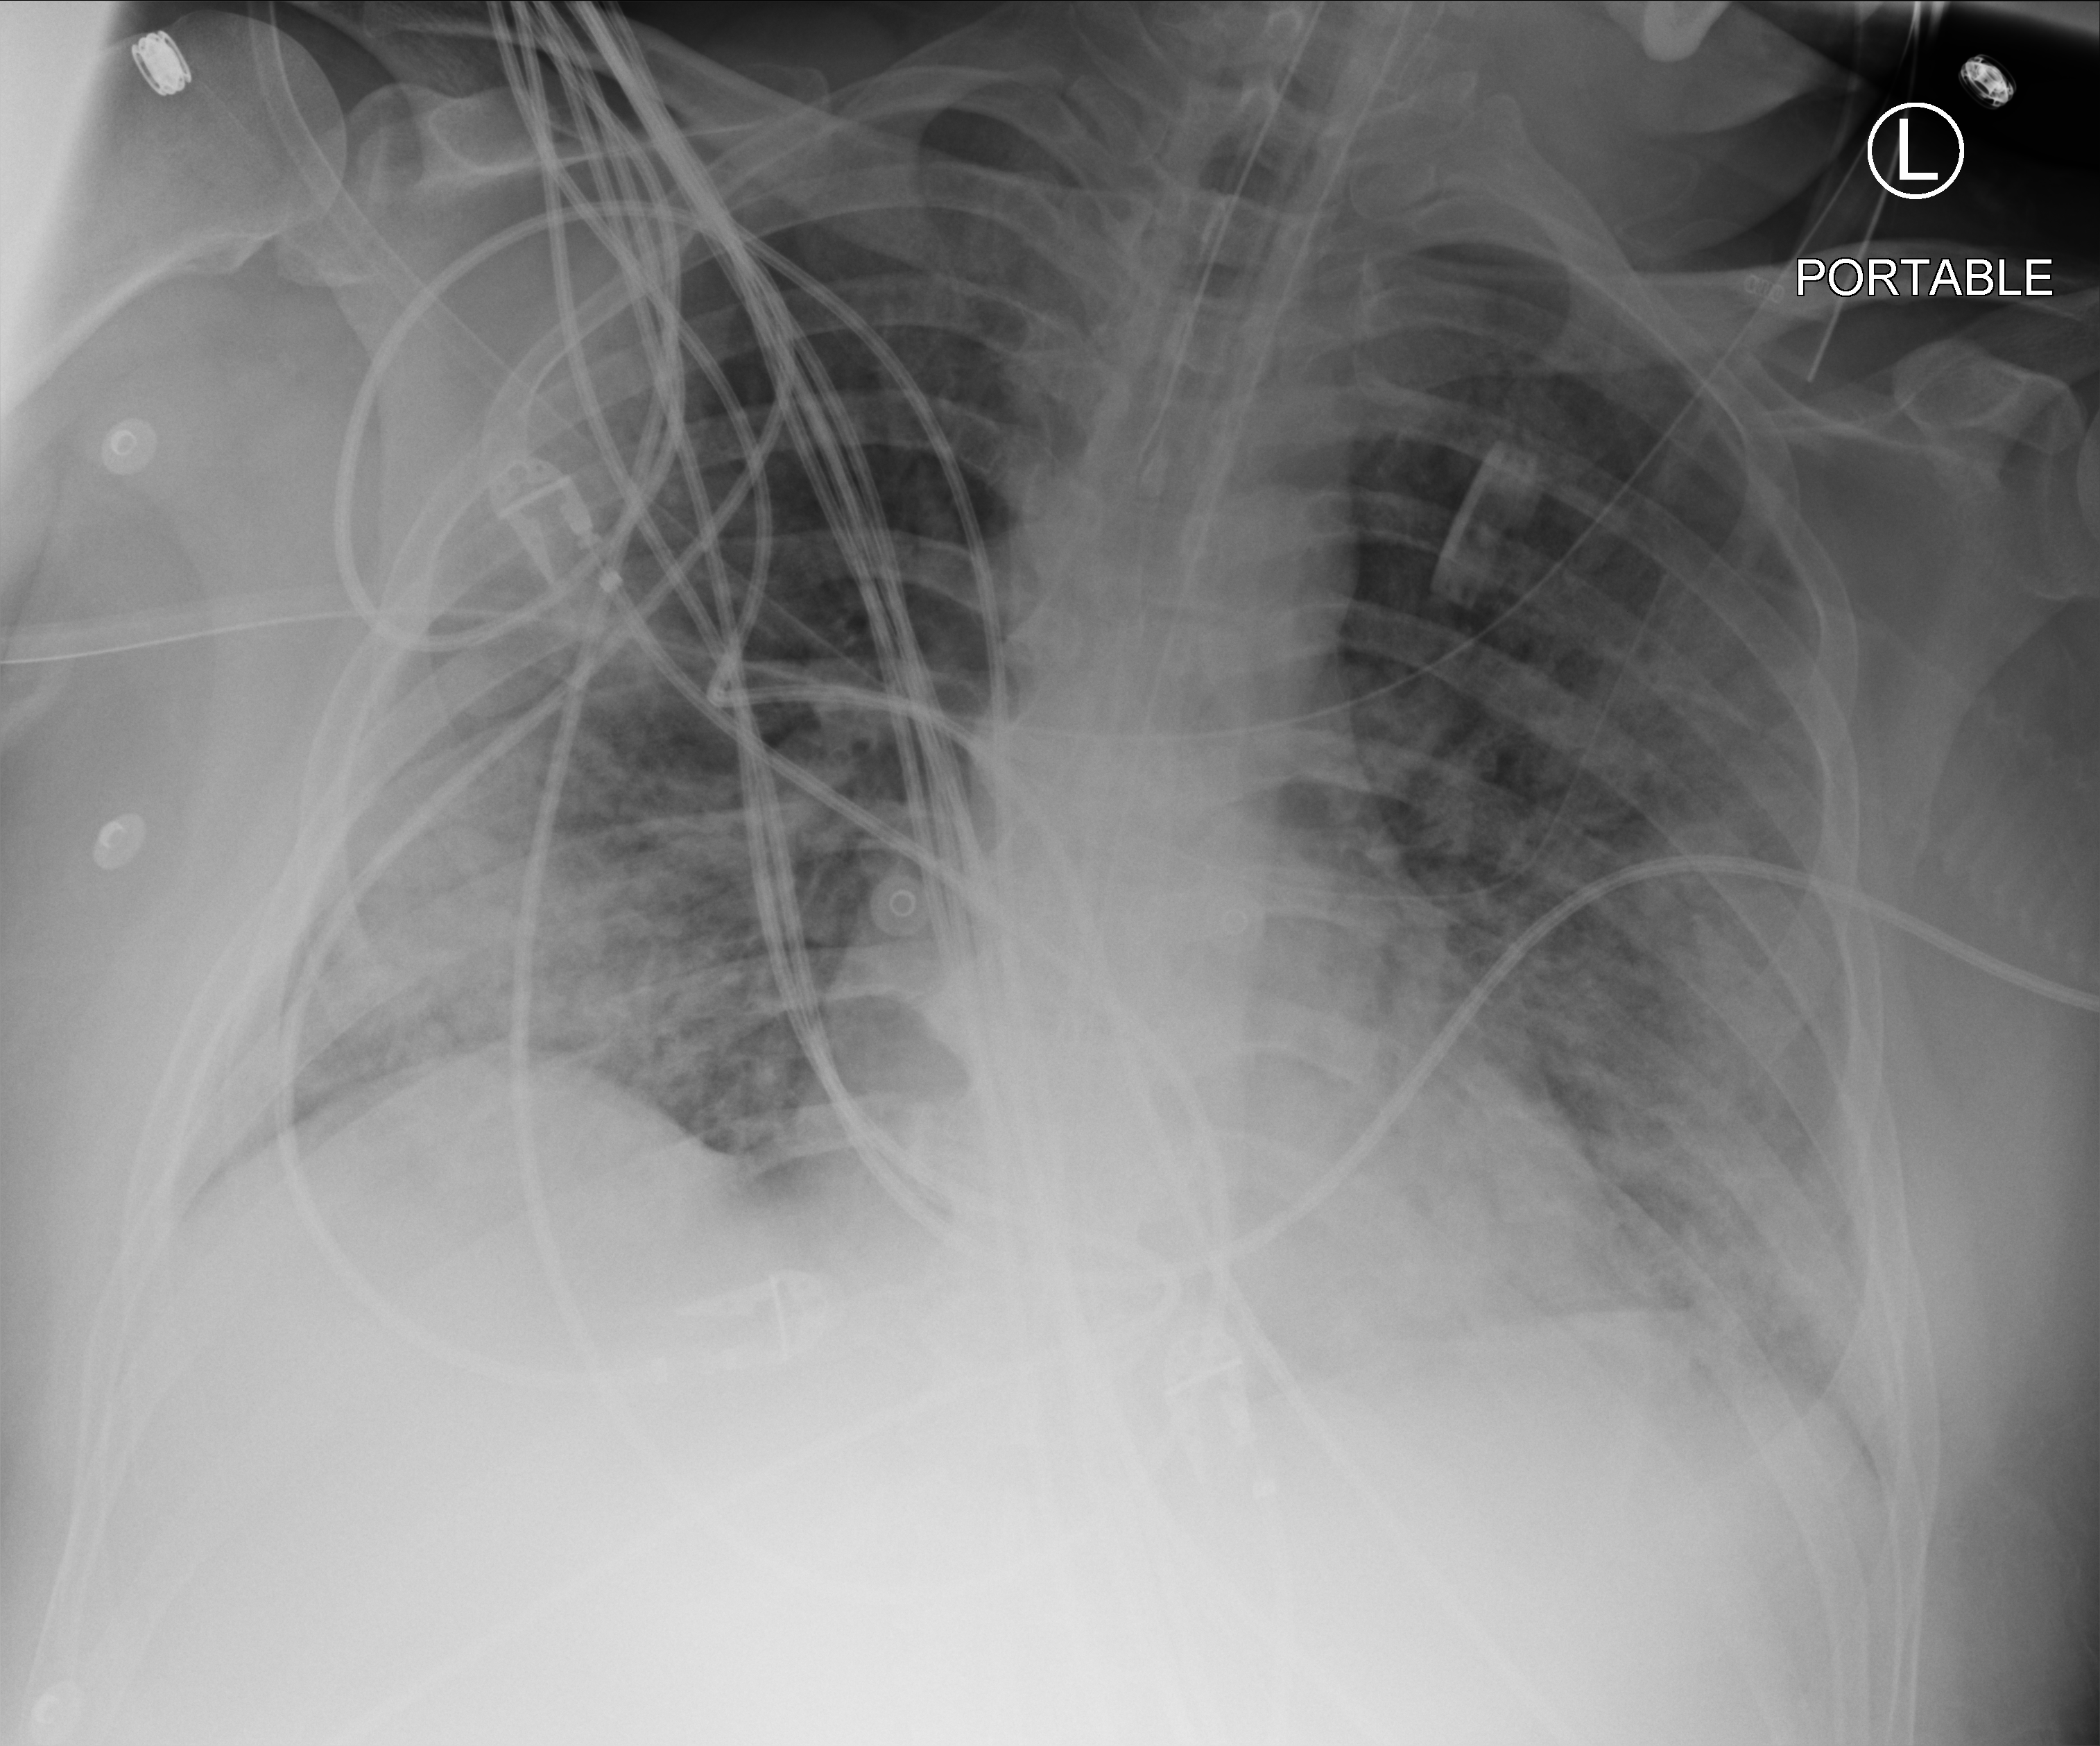
Chest X-ray (portable). Patient hospitalised with COVID-19; male, aged 18–59 years.
Hospital-stay facts (about this admission, not read from this image; timing relative to this image not recorded):
- admitted to intensive care during this hospital stay: yes